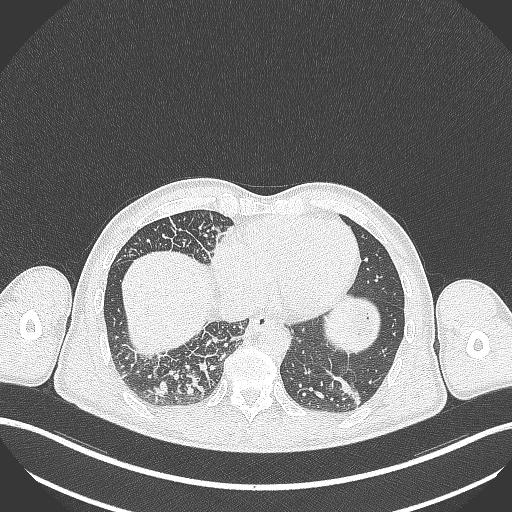
Chest CT, one axial slice. Slice 82 of 348 in the series (ordered by position). Reconstruction kernel B70f. Lung window (W 1500 / L -600 HU). 1 mm slice thickness. 512 × 512 image matrix. Patient: male, 49 years. From the clinical record (not read from this slice): clinical TNM (as recorded): T2b N1 M0.
Outlined on this slice (rectangle marked by the reading radiologist):
- lung tumour (recorded histology: adenocarcinoma): bounding box <332,373,364,410> (left, top, right, bottom; pixels)